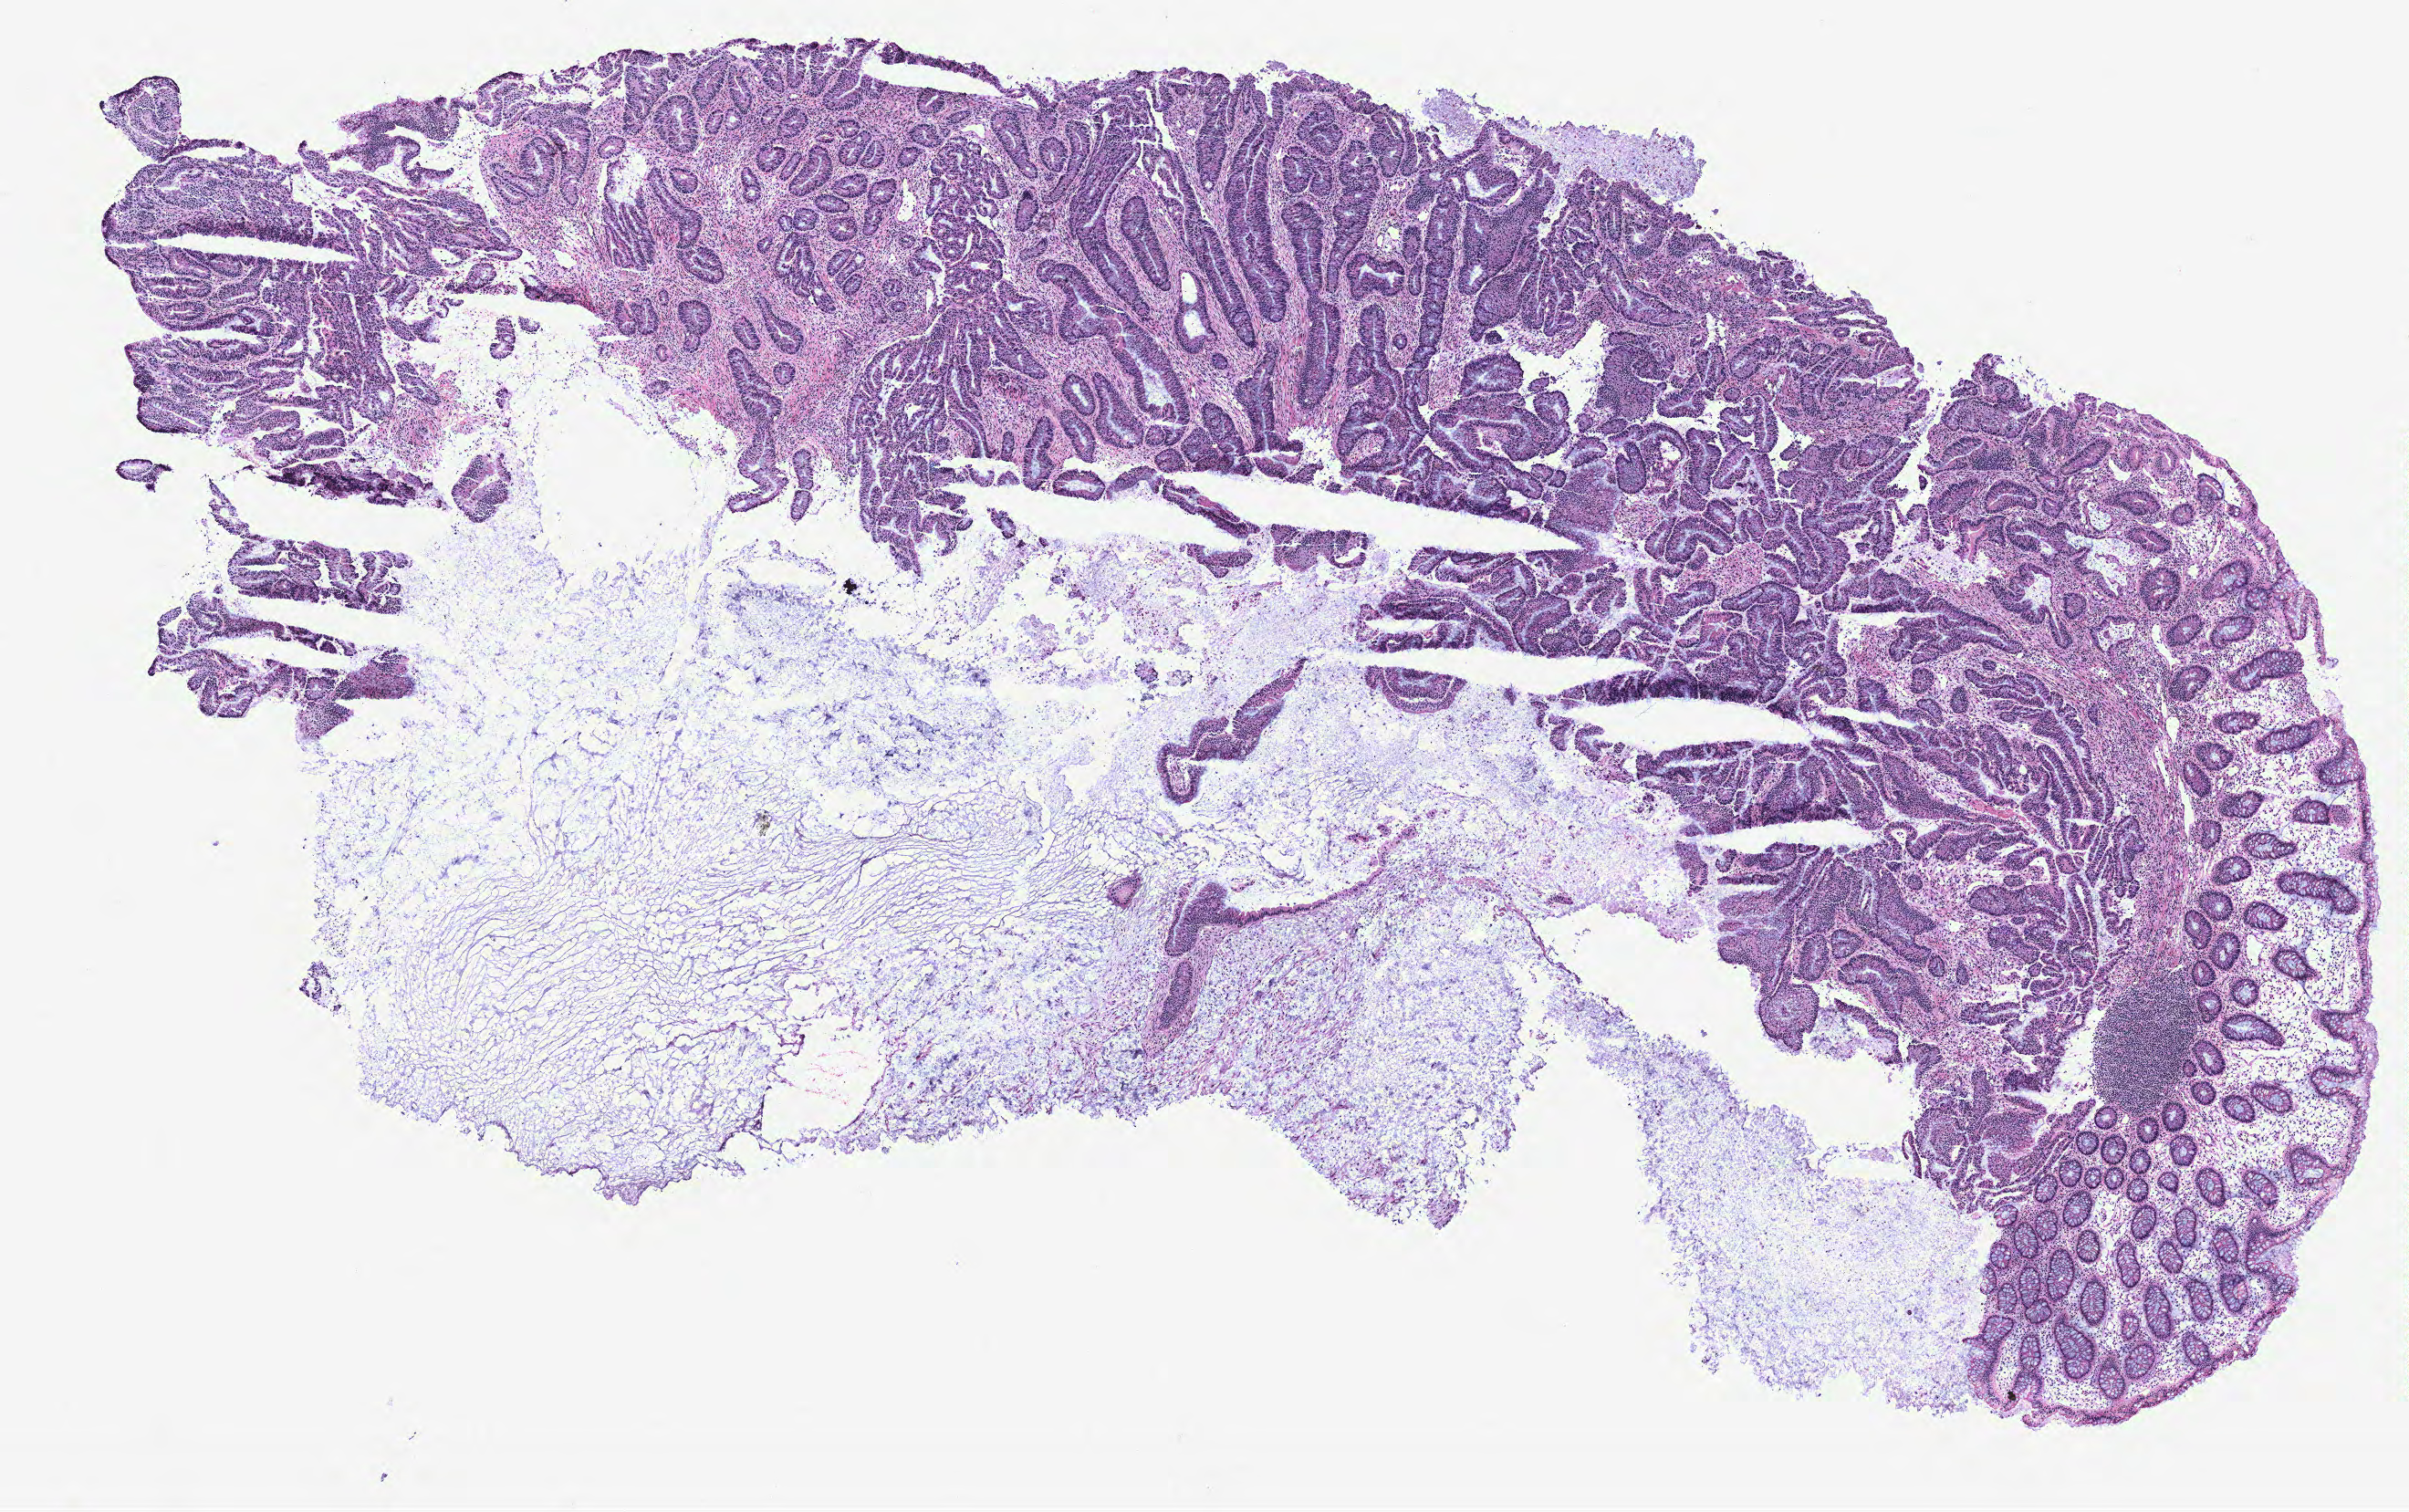
Digitized Hematoxylin and eosin (H&E) stained tissue section (whole slide), whole scanned area (about 10.6 x 6.6 mm) shown as a low-resolution overview; colon, tissue type not recorded.
Patient diagnosis (cohort enrolment): colon cancer (colon).